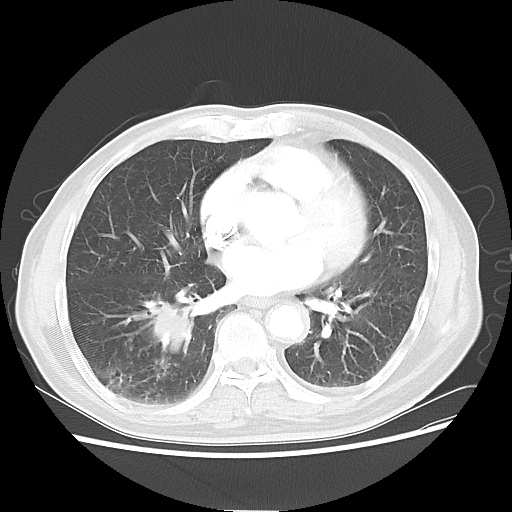
Chest CT, one axial slice; position 26 of 58 along the scan axis; reconstruction kernel LUNG; 120 kVp; lung window (W 1500 / L -600 HU); 5 mm slice thickness; 512 × 512 image matrix, field of view 360 × 360 mm. Patient: male, 74 years. From the clinical record (not read from this slice): clinical TNM (as recorded): T1c N1 M1.
Outlined on this slice (bounding box drawn by a radiologist):
- lung tumour (recorded histology: adenocarcinoma): bounding box [x1, y1, x2, y2] px = [139, 296, 201, 363]